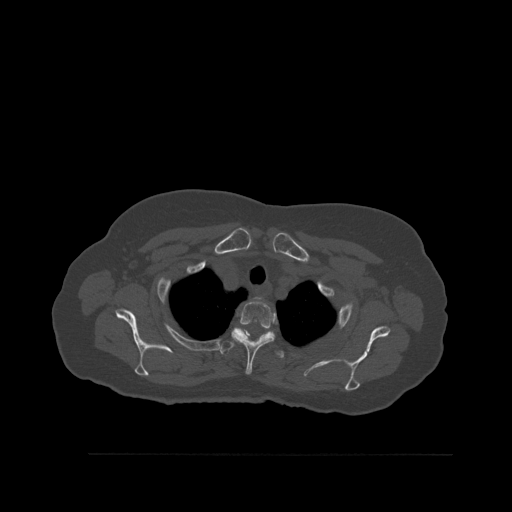
CT including the spine, one axial slice; position 429 of 527 along the scan axis; bone window (W 1800 / L 400 HU); 1.5 mm slice thickness; 512 × 512 image matrix. Female patient, age 73 years. Case-level facts recorded for this patient, not image findings: primary cancer: breast.
Outlined on this slice (semi-automatically segmented with operator editing):
- T2 vertebra: box from (x=231, y=301) to (x=275, y=375) px
- T3 vertebra: (x=220, y=341)–(x=284, y=359)